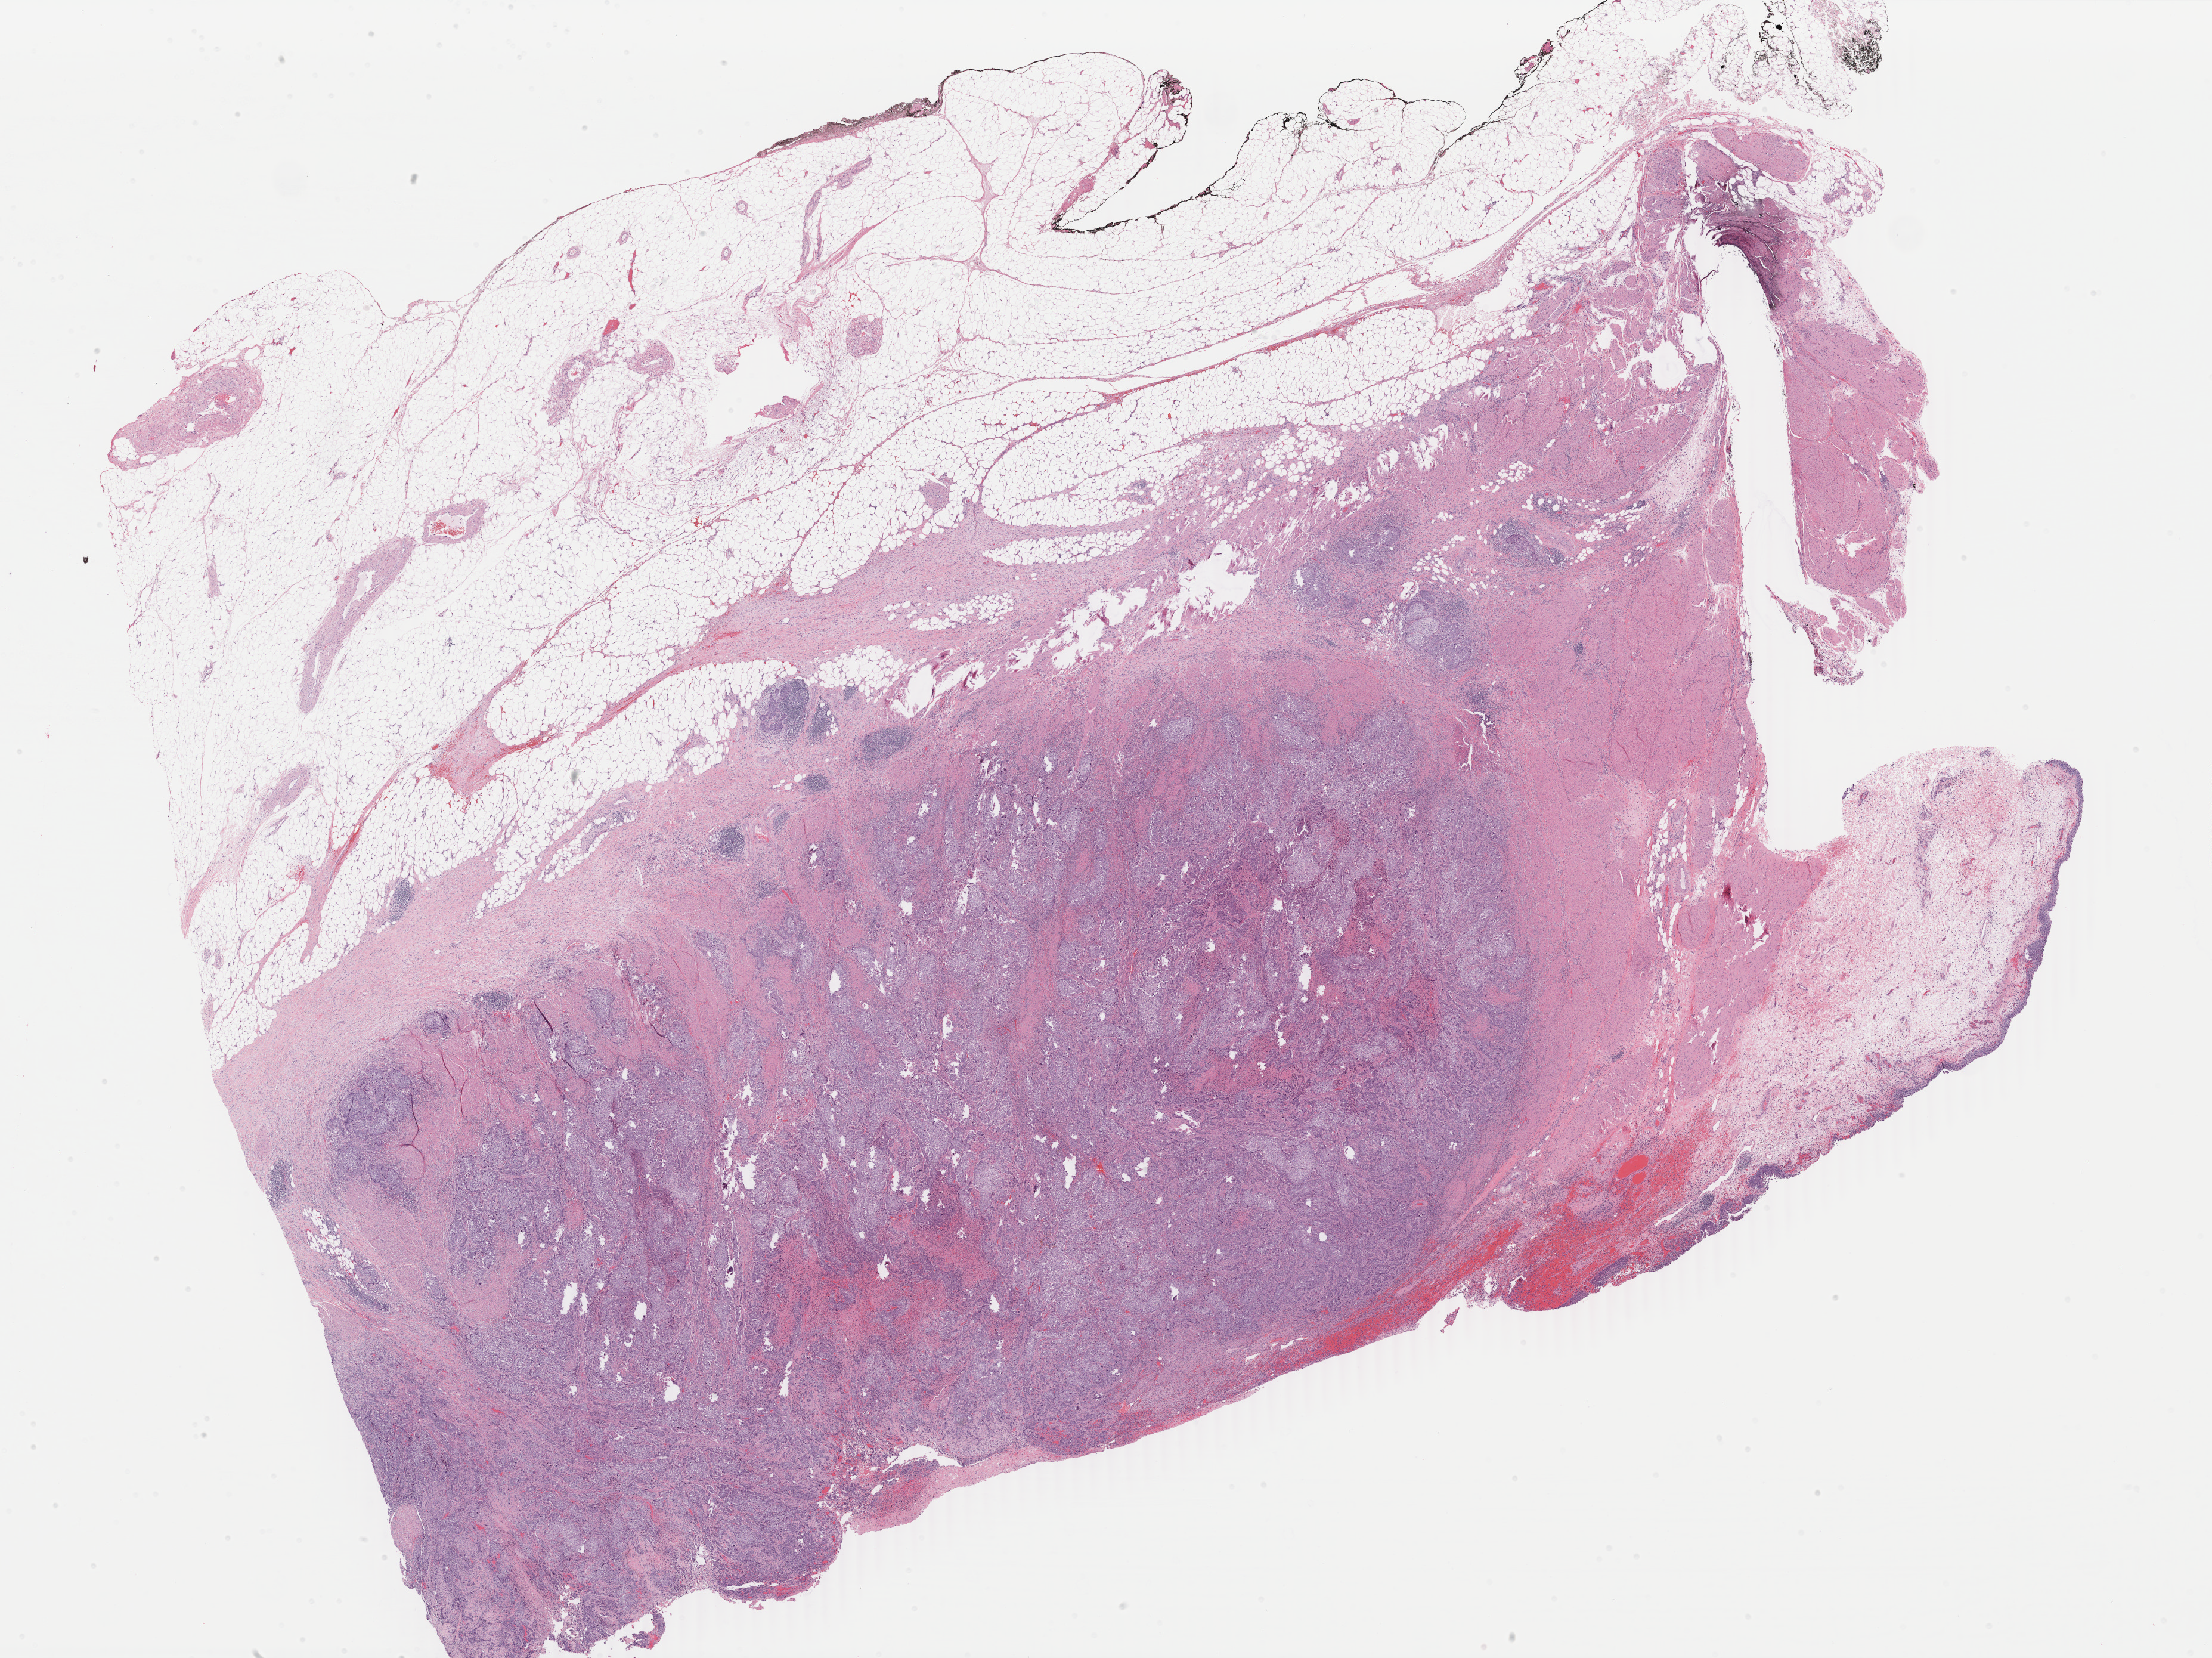
Hematoxylin and eosin (H&E) stained whole-slide image — whole scanned area (about 29.5 x 22.1 mm, acquisition: 40x scan) shown as a low-resolution overview, formalin-fixed paraffin-embedded (FFPE) diagnostic section, bladder, primary tumour sample. Patient: male, age at initial diagnosis 68 years. Histologic grade: high grade.
AJCC pathologic stage: IV (7th edition). Lymph nodes positive (case pathology): 1 of 17 examined. Pathologic diagnosis: Transitional cell carcinoma.